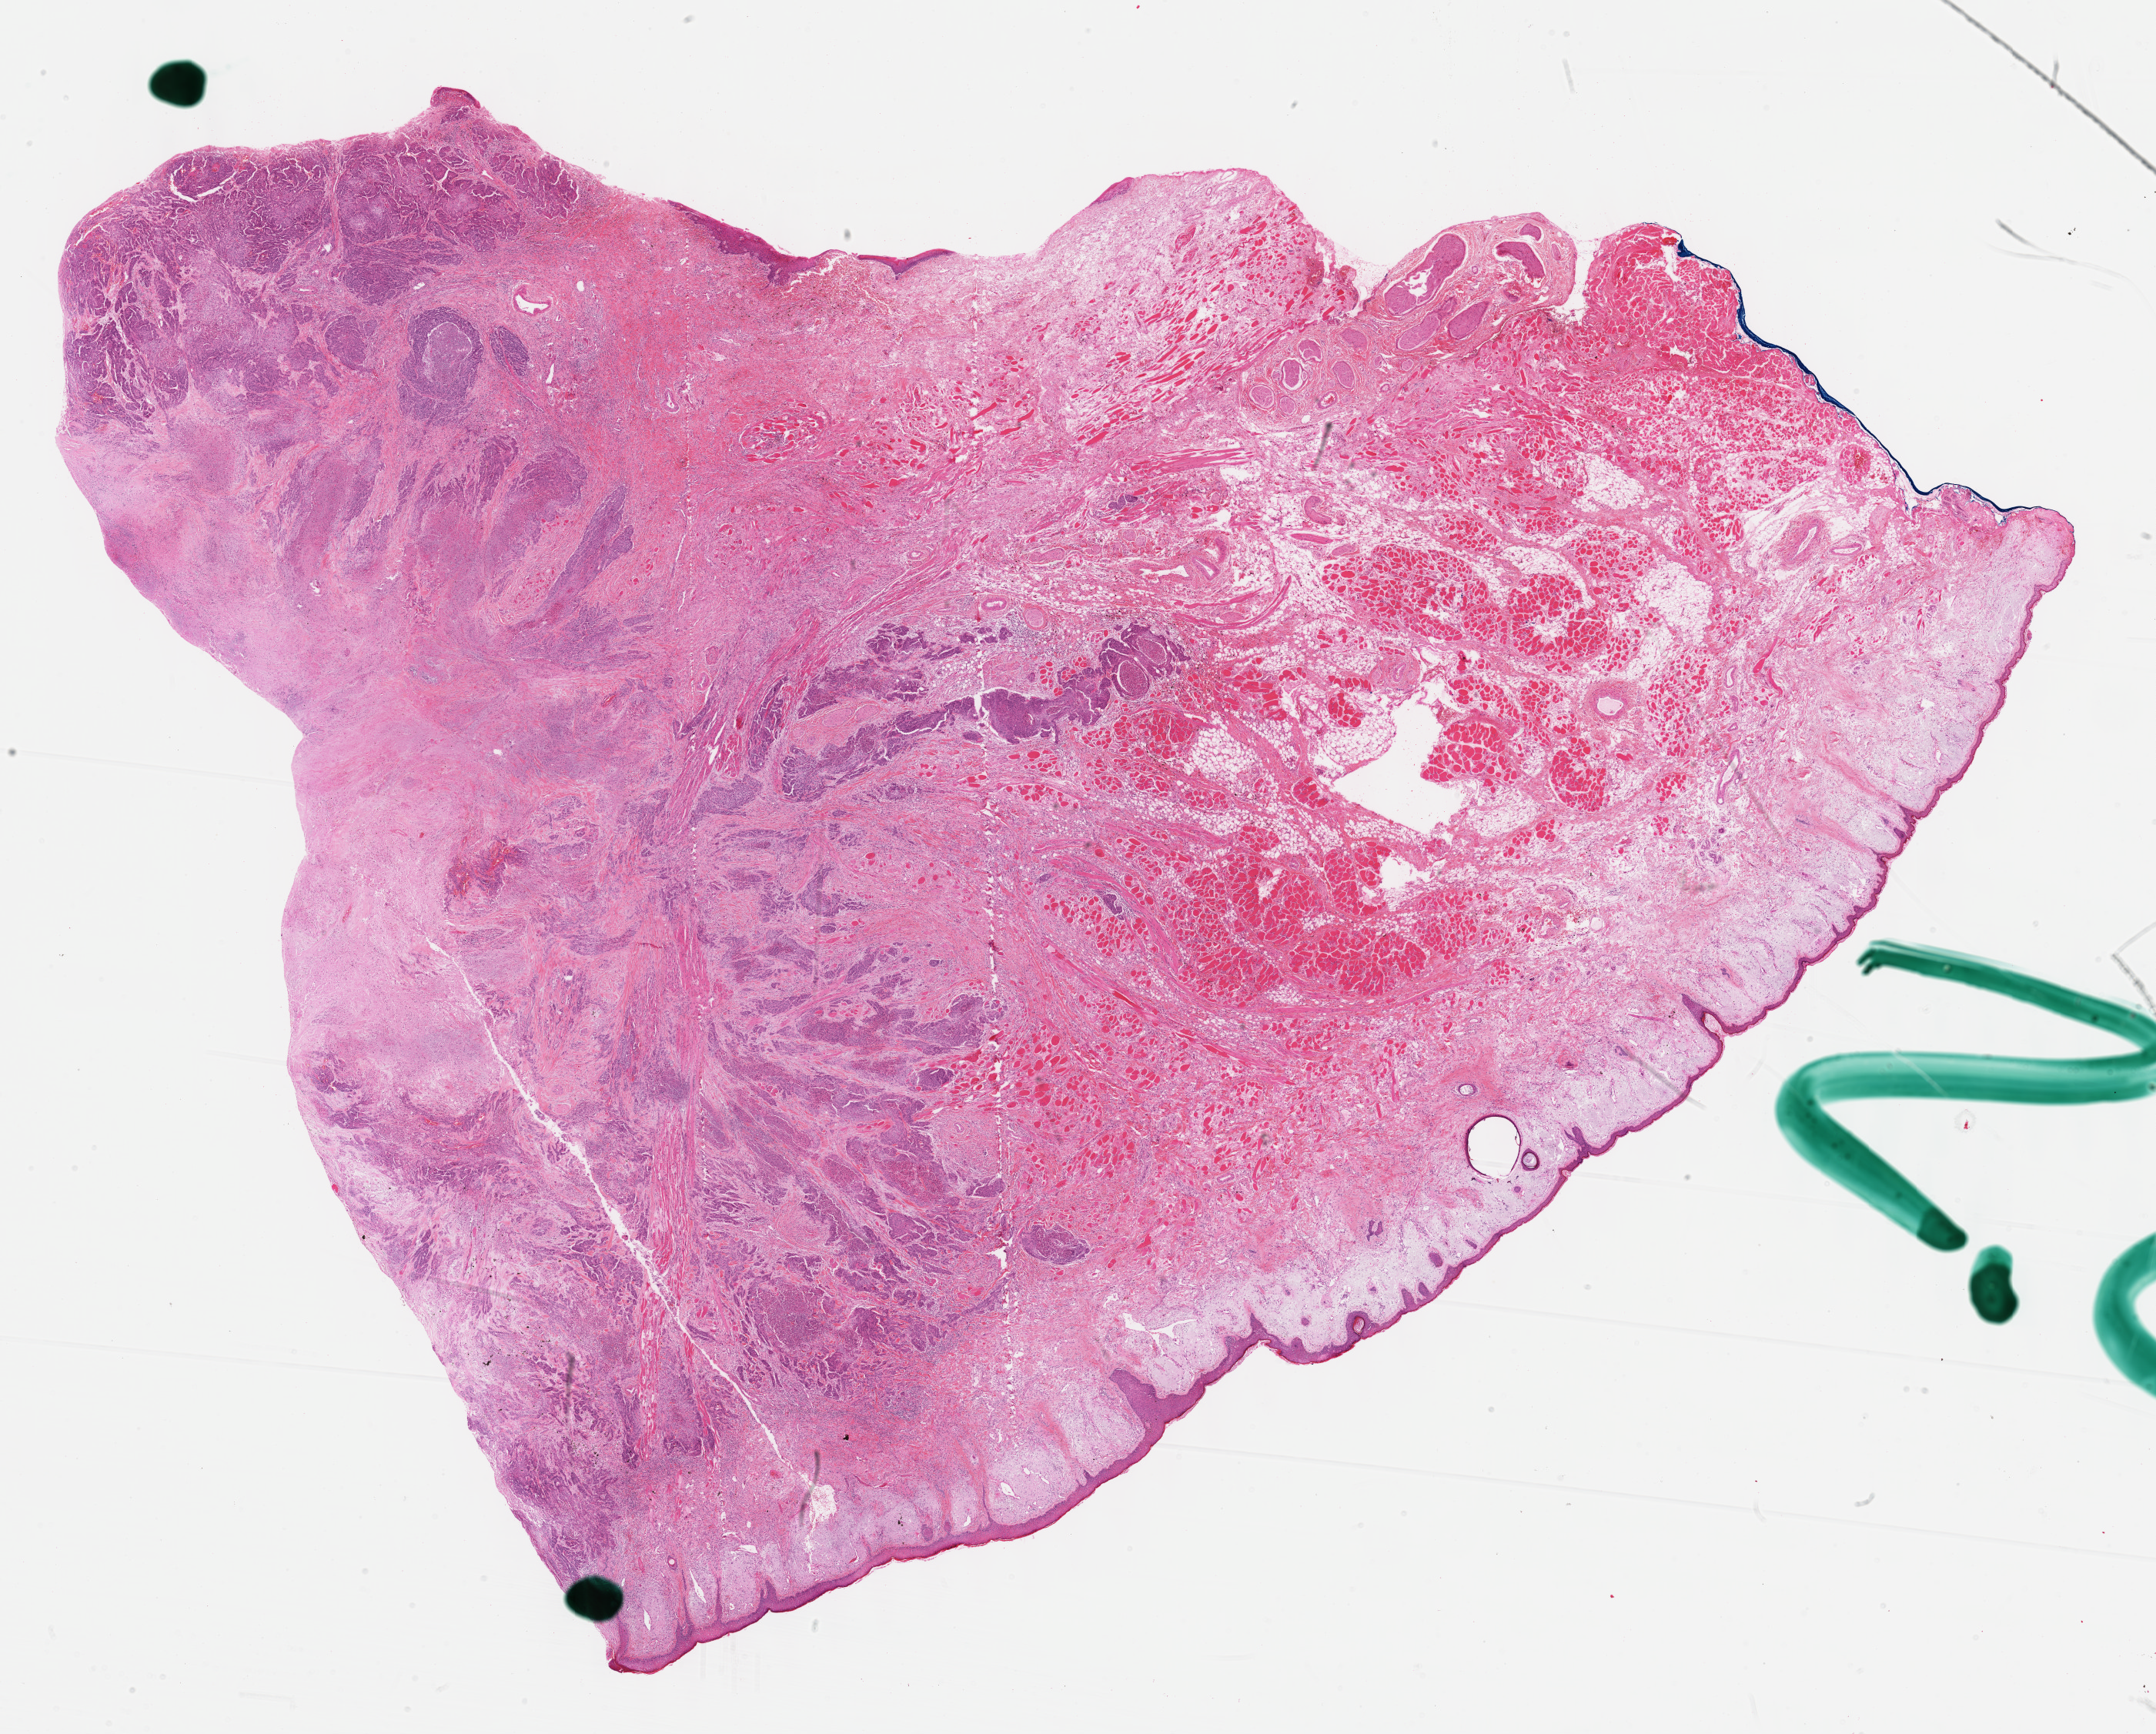
Whole-slide histology image, H&E-stained, a low-resolution overview of the entire scanned area, about 22.6 x 18.2 mm, formalin-fixed paraffin-embedded (FFPE) diagnostic section, head and neck, primary tumour sample. Patient: male, age at initial diagnosis 61 years.
Diagnosis: Squamous cell carcinoma, NOS (tongue, NOS).